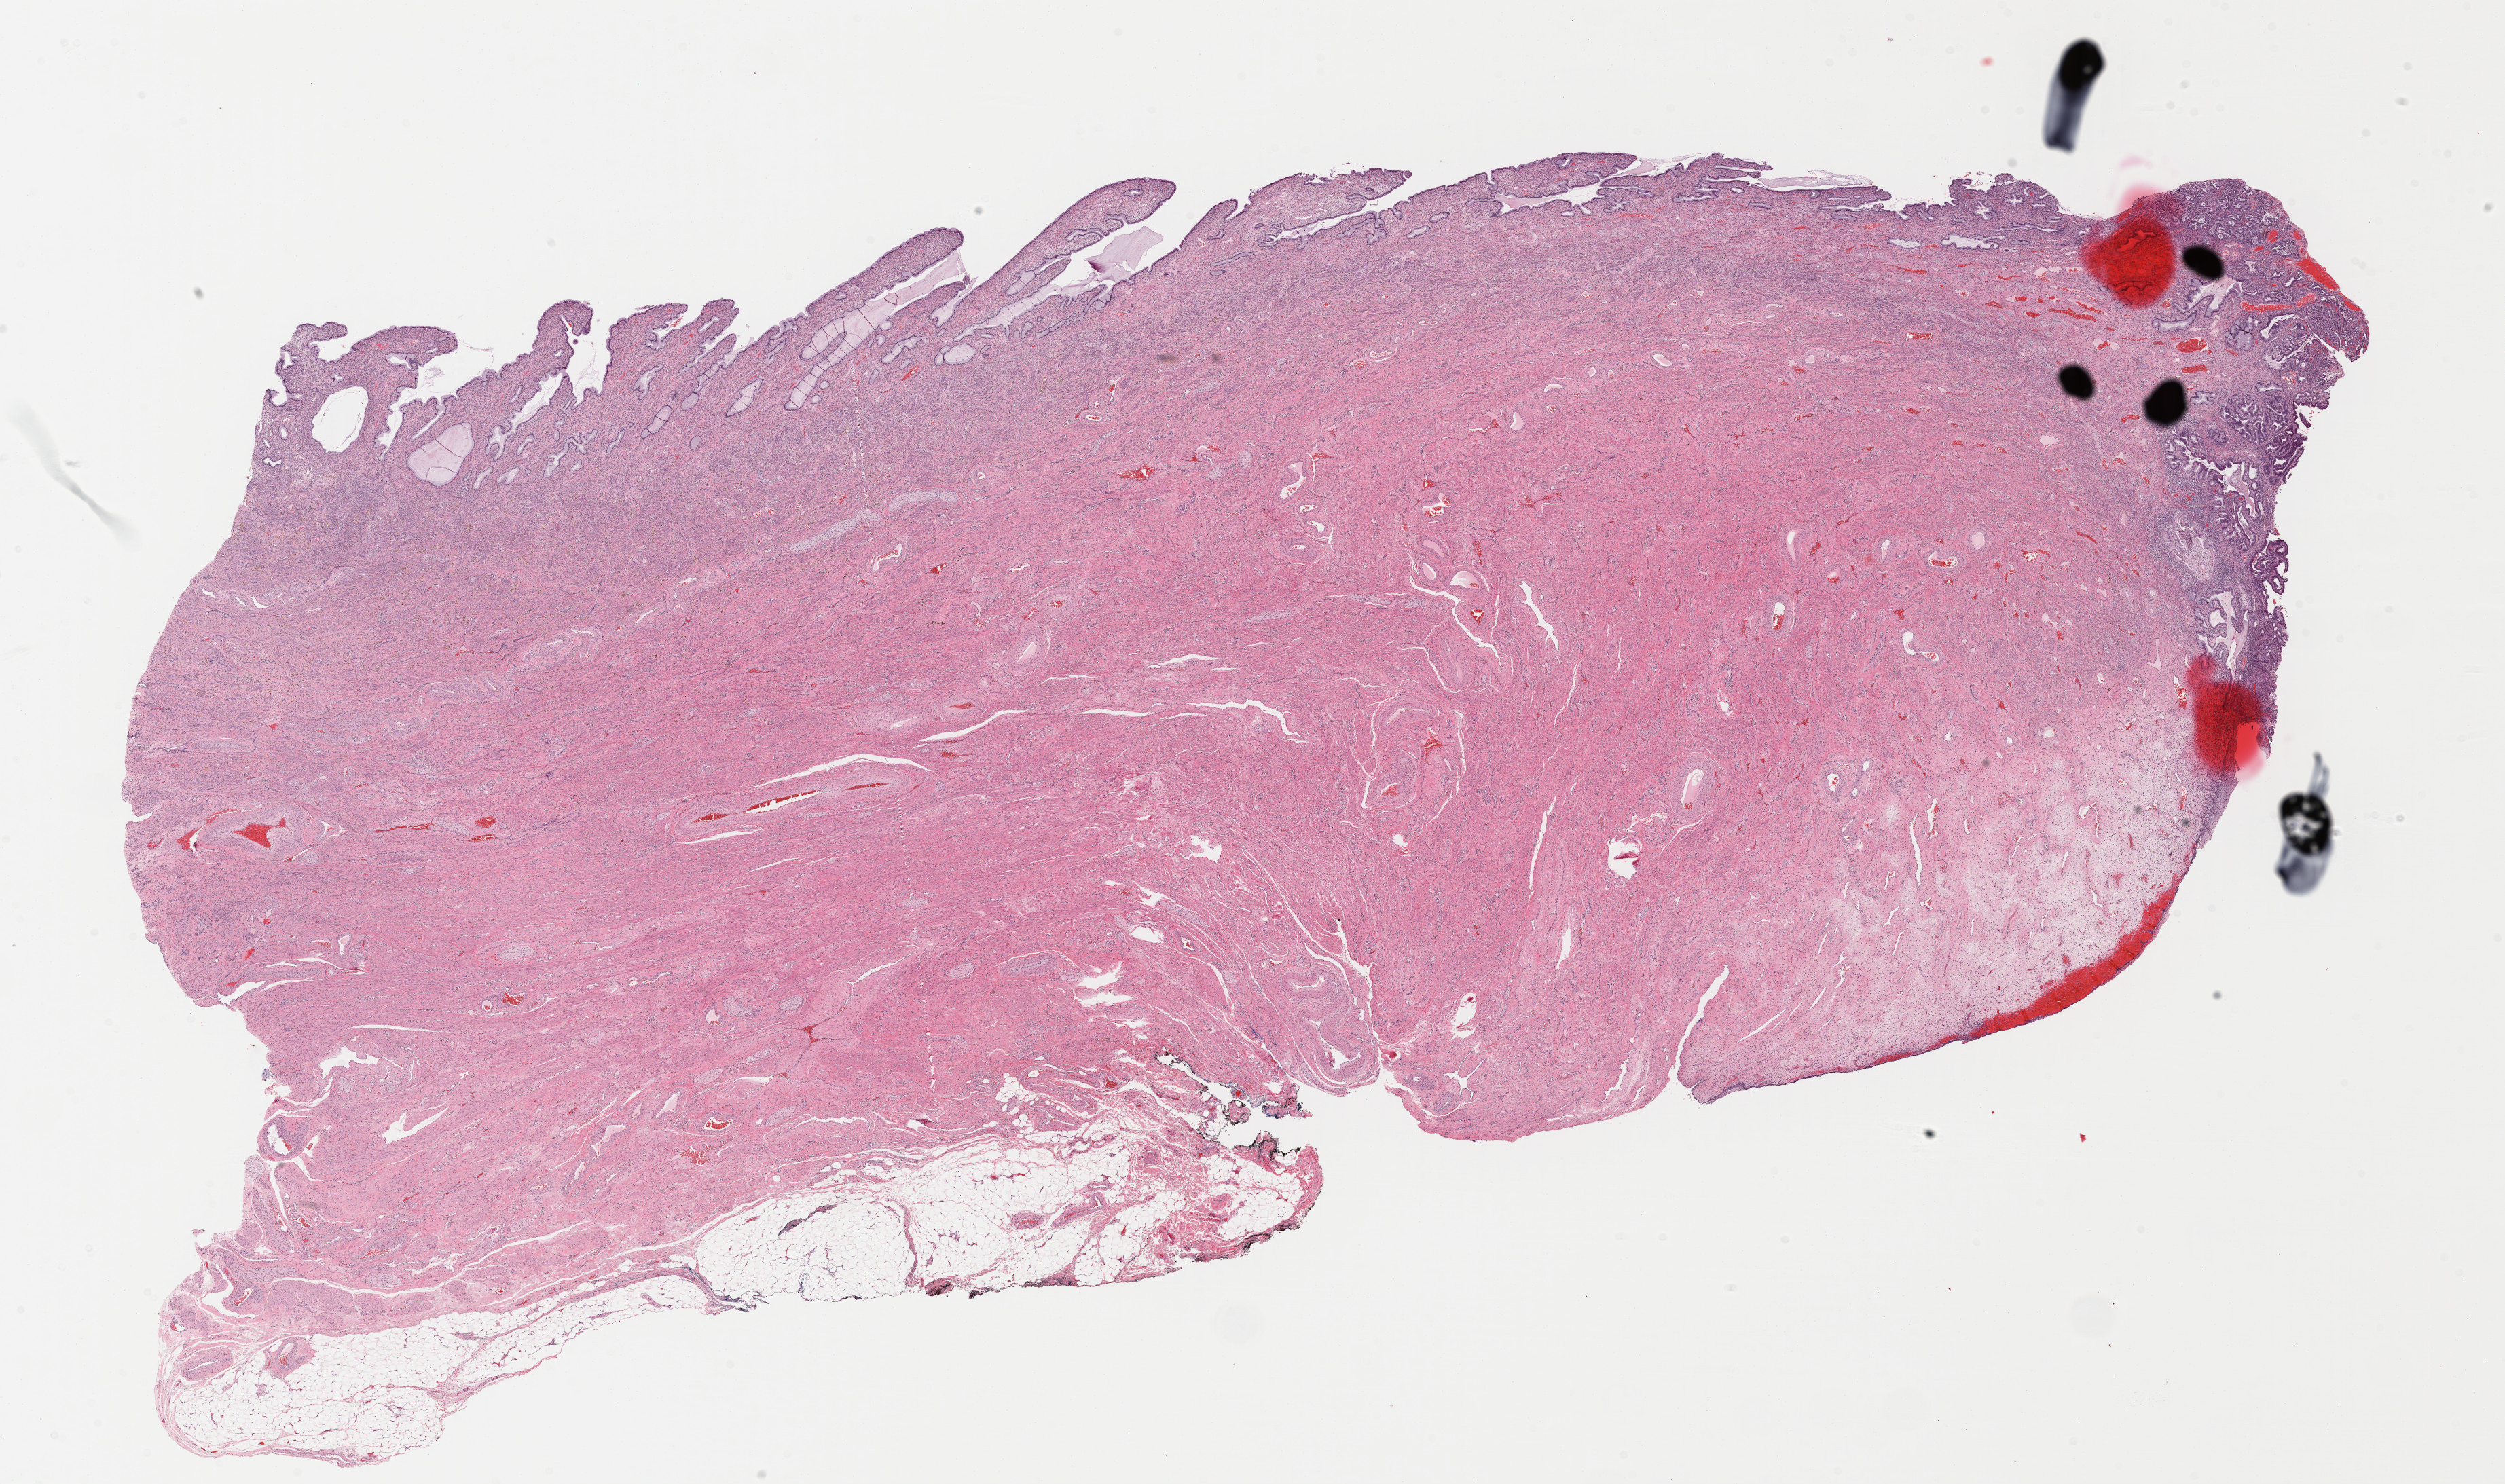
Digitized H&E-stained tissue section (whole slide) — a low-resolution overview of the entire scanned area, about 29.1 x 17.2 mm, FFPE section, cervix, primary tumour sample. Female, age 32 years at initial diagnosis. Histologic grade: G2 (moderately differentiated).
* pathologic diagnosis: Mucinous adenocarcinoma, endocervical type
* FIGO stage: IB1